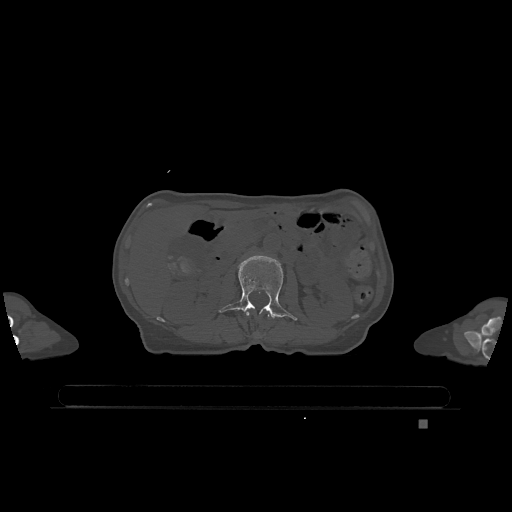
CT including the spine, one axial slice. Slice 421 of 1317 in the series (ordered by position). Bone window (W 1800 / L 400 HU). 0.5 mm slice thickness. 512 × 512 image matrix, field of view 500 × 500 mm. Female patient, age 74 years. From the clinical record (not read from this slice): primary cancer: lung; vertebrae with lytic lesions (as recorded): T1, T4, T5, T6, L4, L5.
Annotated regions visible in this slice (semi-automatically segmented with operator editing):
- L1 vertebra: box from (x=246, y=312) to (x=270, y=317) px
- L2 vertebra: (x=218, y=255)–(x=297, y=321)